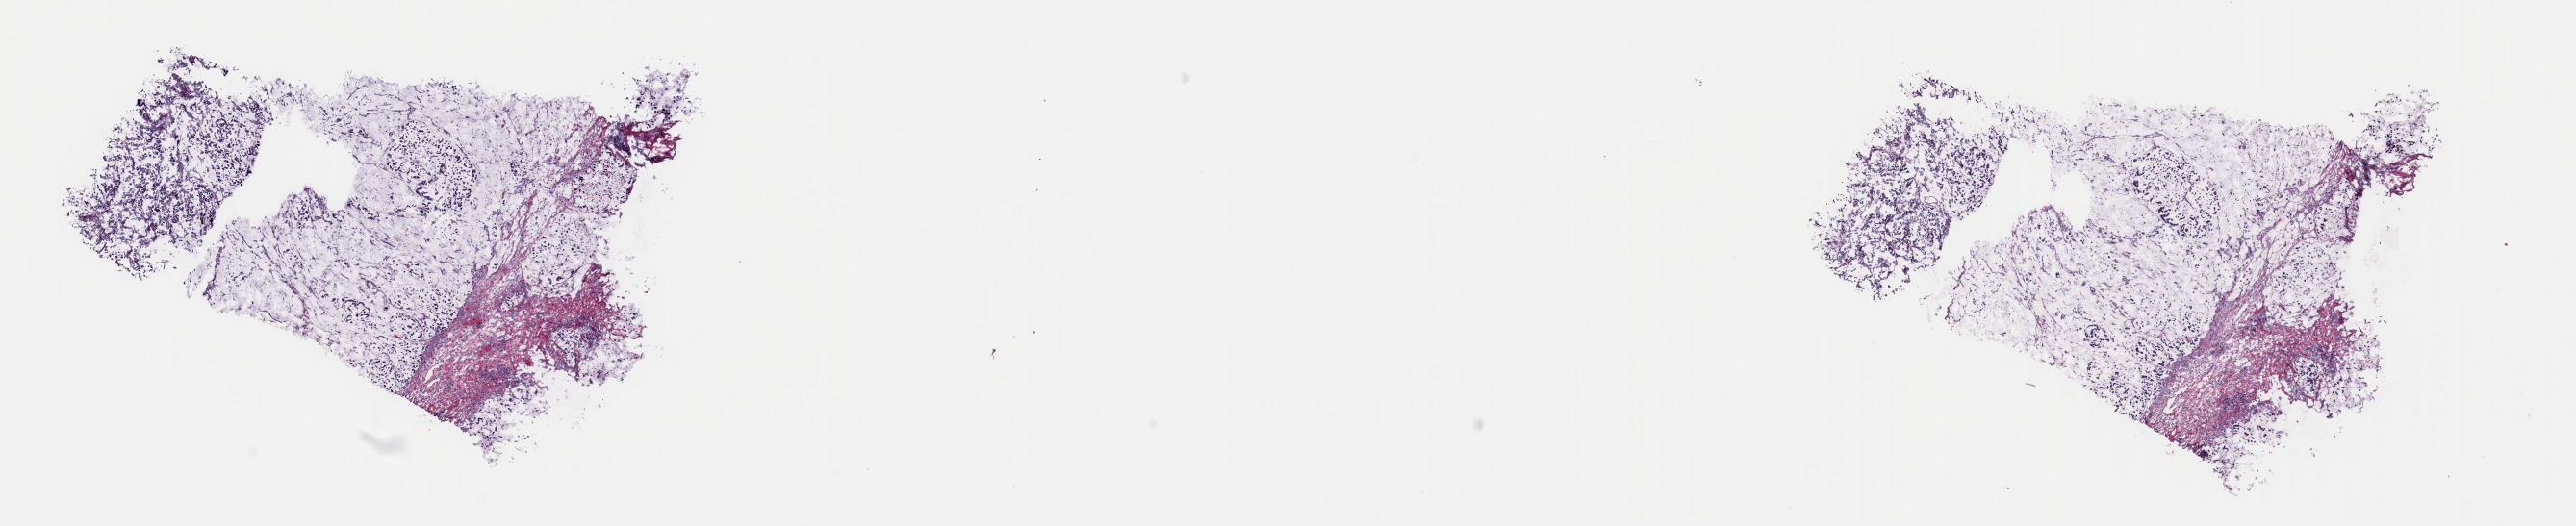
Whole-slide histology image, H&E-stained — low-resolution overview of the scanned area, about 21.1 x 4.3 mm. Frozen section from the top of the tissue portion. Sample: primary tumour, esophagus. Patient: male, age at initial diagnosis 81 years. Histologic grade: GX (grade cannot be assessed). Pathologist review of this section (percent, as recorded): tumour cells 80%, tumour nuclei 85%, normal cells 0%, stromal cells 18%, necrosis 2%. Infiltration values recorded for this section: lymphocyte infiltration 2%, monocyte infiltration 0%, neutrophil infiltration 0%.
Lymph nodes positive (case pathology): 12 of 21 examined. Diagnosis: Mucinous adenocarcinoma (lower third of esophagus).